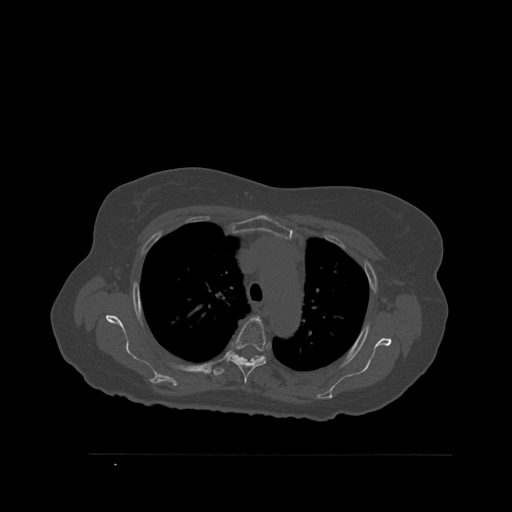
CT including the spine, one axial slice; slice 406 of 527 in the series (ordered by position); bone window (W 1800 / L 400 HU); 1.5 mm slice thickness; 512 × 512 image matrix, field of view 470 × 470 mm. Patient: female, 73 years. Case-level facts recorded for this patient, not image findings: primary cancer: breast; vertebrae with lytic lesions (as recorded): L2.
Outlined on this slice (semi-automatically segmented with operator editing):
- T4 vertebra: bounding box <226,317,267,384> (left, top, right, bottom; pixels)
- T5 vertebra: <211,354,267,376>